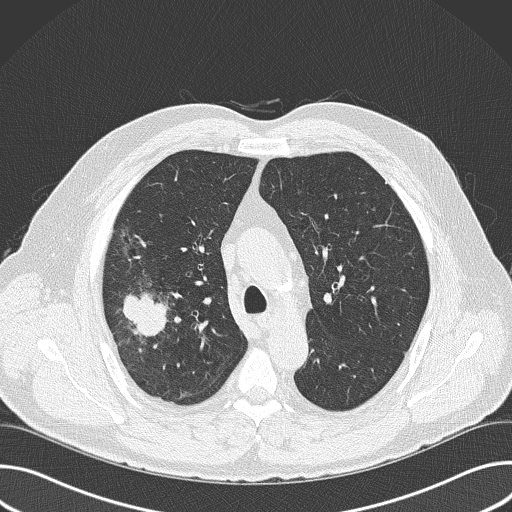
Chest CT (low-dose screening protocol), one axial image, baseline annual screen, lung window (W 1500 / L -600 HU), lung (sharp) reconstruction kernel (B50f), 120 kVp, slice 113 of 157 in the series, 512 × 512 image matrix. Male participant, aged 56 years at enrolment.
Expert-annotated lung lesion, box from (x=83, y=268) to (x=189, y=379) px. Reader record for this screening exam (exam-level; its link to the box is not recorded): non-calcified nodule or mass ≥4 mm, right upper lobe, 6 × 5 mm, spiculated (stellate) margins, soft tissue attenuation. Later outcome: lung cancer diagnosed 16 days after this screen — adenocarcinoma, NOS, right upper lobe, poorly differentiated (G3), stage IIB (AJCC 6th edition), 60 mm at pathology.